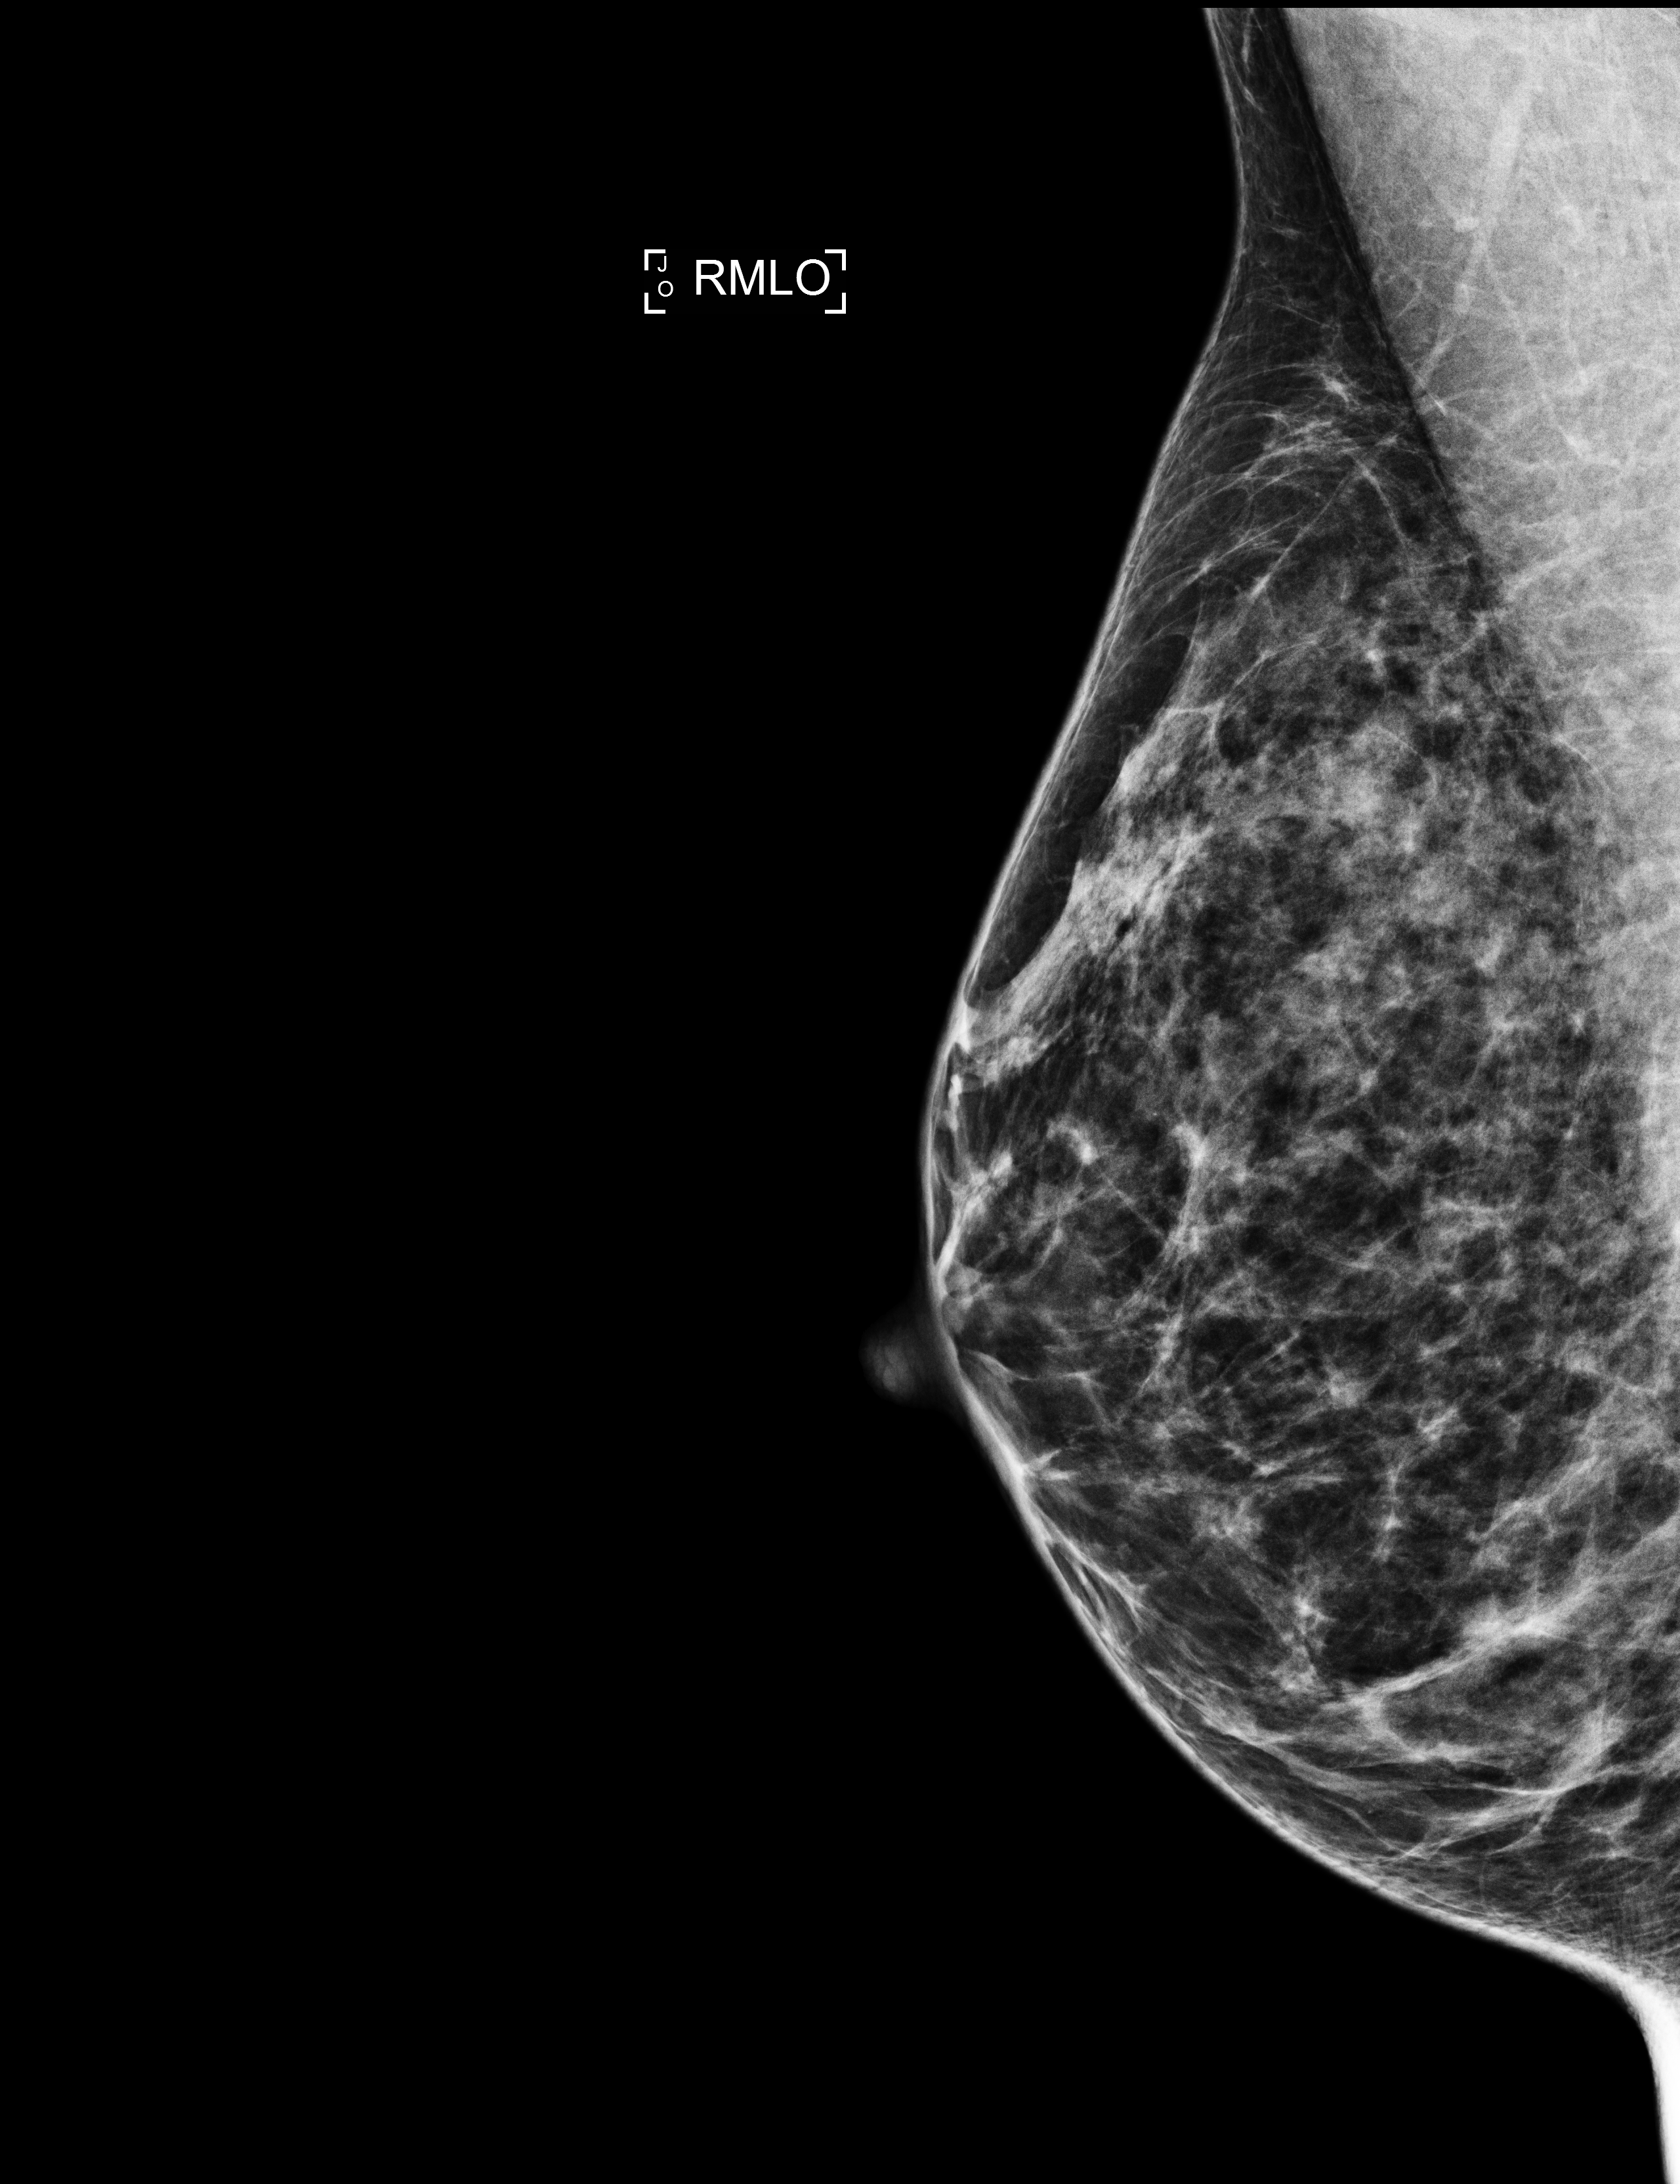
Screening examination, compressed breast thickness 48 mm, system: Selenia Dimensions. Patient: female, 41 years.
Image type: full-field digital mammogram. Breast: right. Projection: medio-lateral oblique projection.